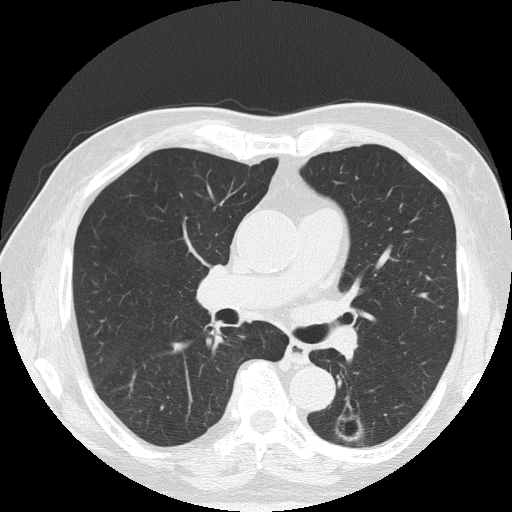
Axial slice from a low-dose chest CT screening exam; baseline screening round; lung window (W 1500 / L -600 HU); slice 72 of 145 in the series. Male, age 71 years at enrolment.
• Expert-annotated lung lesion, bounding box <321,409,376,453> (left, top, right, bottom; pixels).
• Screening reader's record for this exam: no non-calcified nodule ≥4 mm recorded.
• Official screen result: negative screen, significant abnormalities not suspicious for lung cancer.
• Later outcome: lung cancer diagnosed 340 days after this screen — adenocarcinoma, NOS, left lower lobe, poorly differentiated (G3), stage IA (AJCC 6th edition), 28 mm at pathology.